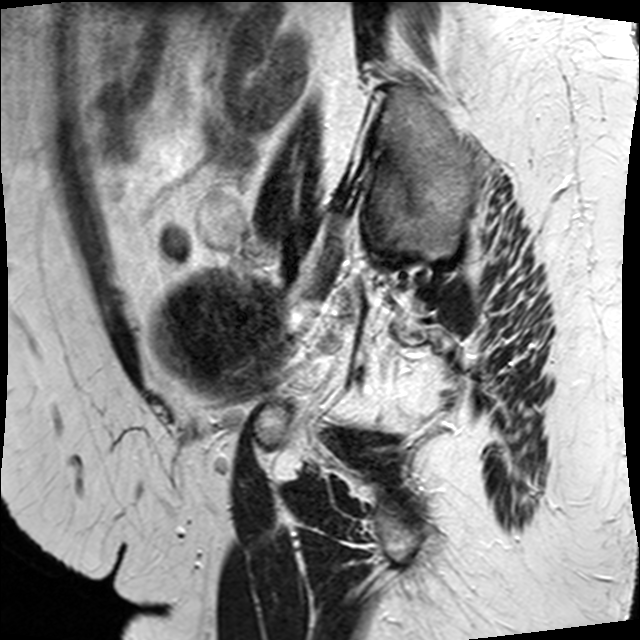
Pelvic MRI for cervical cancer, one sagittal slice. Position 7 of 34 along the scan axis. T2-weighted. 1.5 T. TE 89 ms, TR 3320 ms. 4 mm slice thickness. 640 × 640 image matrix, field of view 260 × 260 mm. Patient: female, 50 years.
Annotated regions visible in this slice (manually delineated by an expert):
- uterus and cervix: bounding box (x1, y1, x2, y2) in pixels: (143, 269, 290, 397)